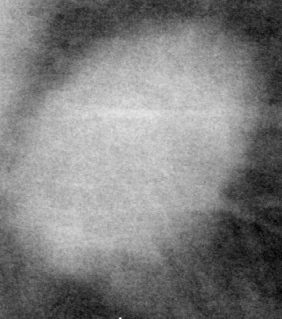
Crop from a digitized film mammogram around one marked abnormality; left breast; MLO view; BI-RADS breast density category 2 (scale 1–4).
- Marked abnormality: mass, shape oval, margins spiculated; BI-RADS assessment category 4; pathology result (as recorded, not read from the image): malignant.